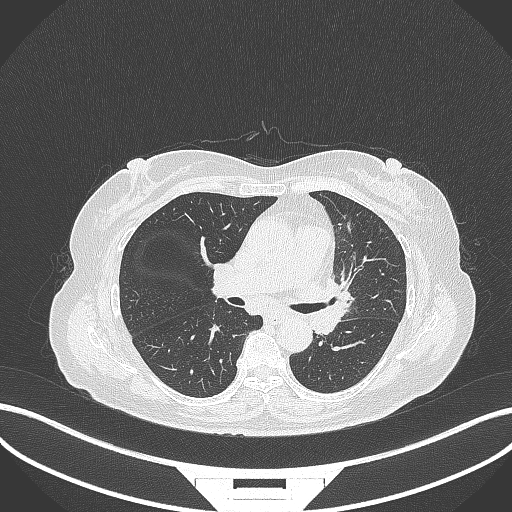
Chest CT, one axial slice; position 189 of 382 along the scan axis; reconstruction kernel B70f; 120 kVp; lung window (W 1500 / L -600 HU); 1 mm slice thickness; 512 × 512 image matrix, field of view 400 × 400 mm. Female patient, age 64 years. Case-level facts recorded for this patient, not image findings: clinical TNM (as recorded): T2a N2 M0.
Structures marked on this image (bounding box drawn by a radiologist):
- lung tumour (recorded histology: adenocarcinoma): bounding box [x1, y1, x2, y2] px = [310, 277, 351, 341]